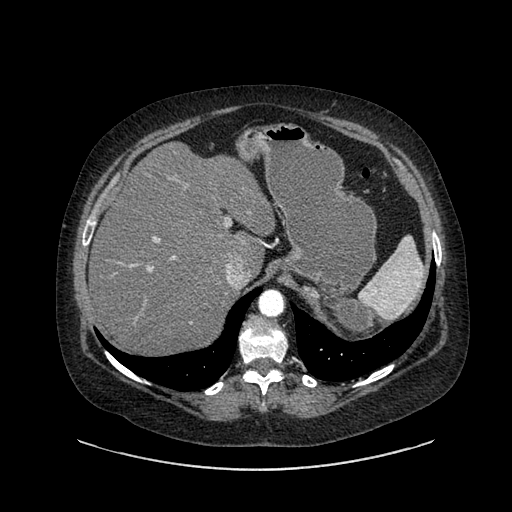
Contrast-enhanced abdominal CT, one axial slice; slice 638 of 769 in the series (ordered by position); intravenous contrast given; soft-tissue window (W 400 / L 40 HU); 0.62 mm slice thickness; 512 × 512 image matrix. Female patient, age 61 years. Case-level facts recorded for this patient, not image findings: diagnosis: adrenocortical carcinoma; tumour side: left adrenal; tumour size at pathology: 13 cm; Ki-67 index: 79 %; stage (as recorded): 2.
Annotated regions visible in this slice (semi-automatic segmentation, software-assisted and operator-edited):
- mass: bounding box (x1, y1, x2, y2) in pixels: (314, 291, 376, 338)